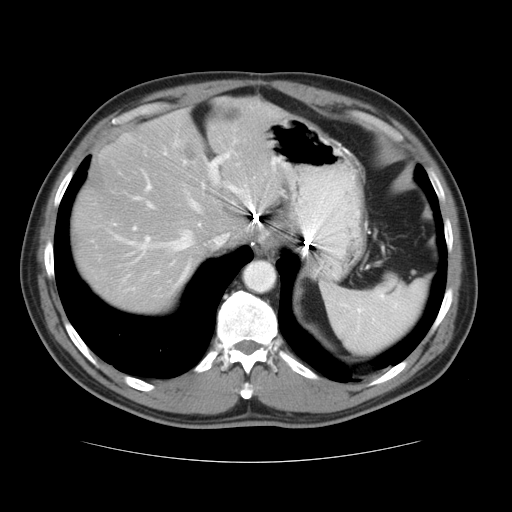
Contrast-enhanced abdominal CT, one axial slice; slice 28 of 37 in the series (ordered by position); reconstruction kernel STANDARD; intravenous contrast given; soft-tissue window (W 400 / L 40 HU); 5 mm slice thickness; 512 × 512 image matrix. Male patient, age 66 years. Case-level facts recorded for this patient, not image findings: diagnosis: colorectal cancer liver metastases, imaged before liver resection; multiple liver metastases: yes.
Structures marked on this image (expert manual segmentation):
- hepatic veins: bounding box [x1, y1, x2, y2] px = [121, 184, 254, 255]
- liver: [71, 102, 287, 315]
- planned liver remnant (the part of the liver to remain after resection): [71, 106, 287, 315]
- portal vein (with intrahepatic branches): [133, 153, 230, 231]
- liver metastasis: [177, 142, 201, 166]